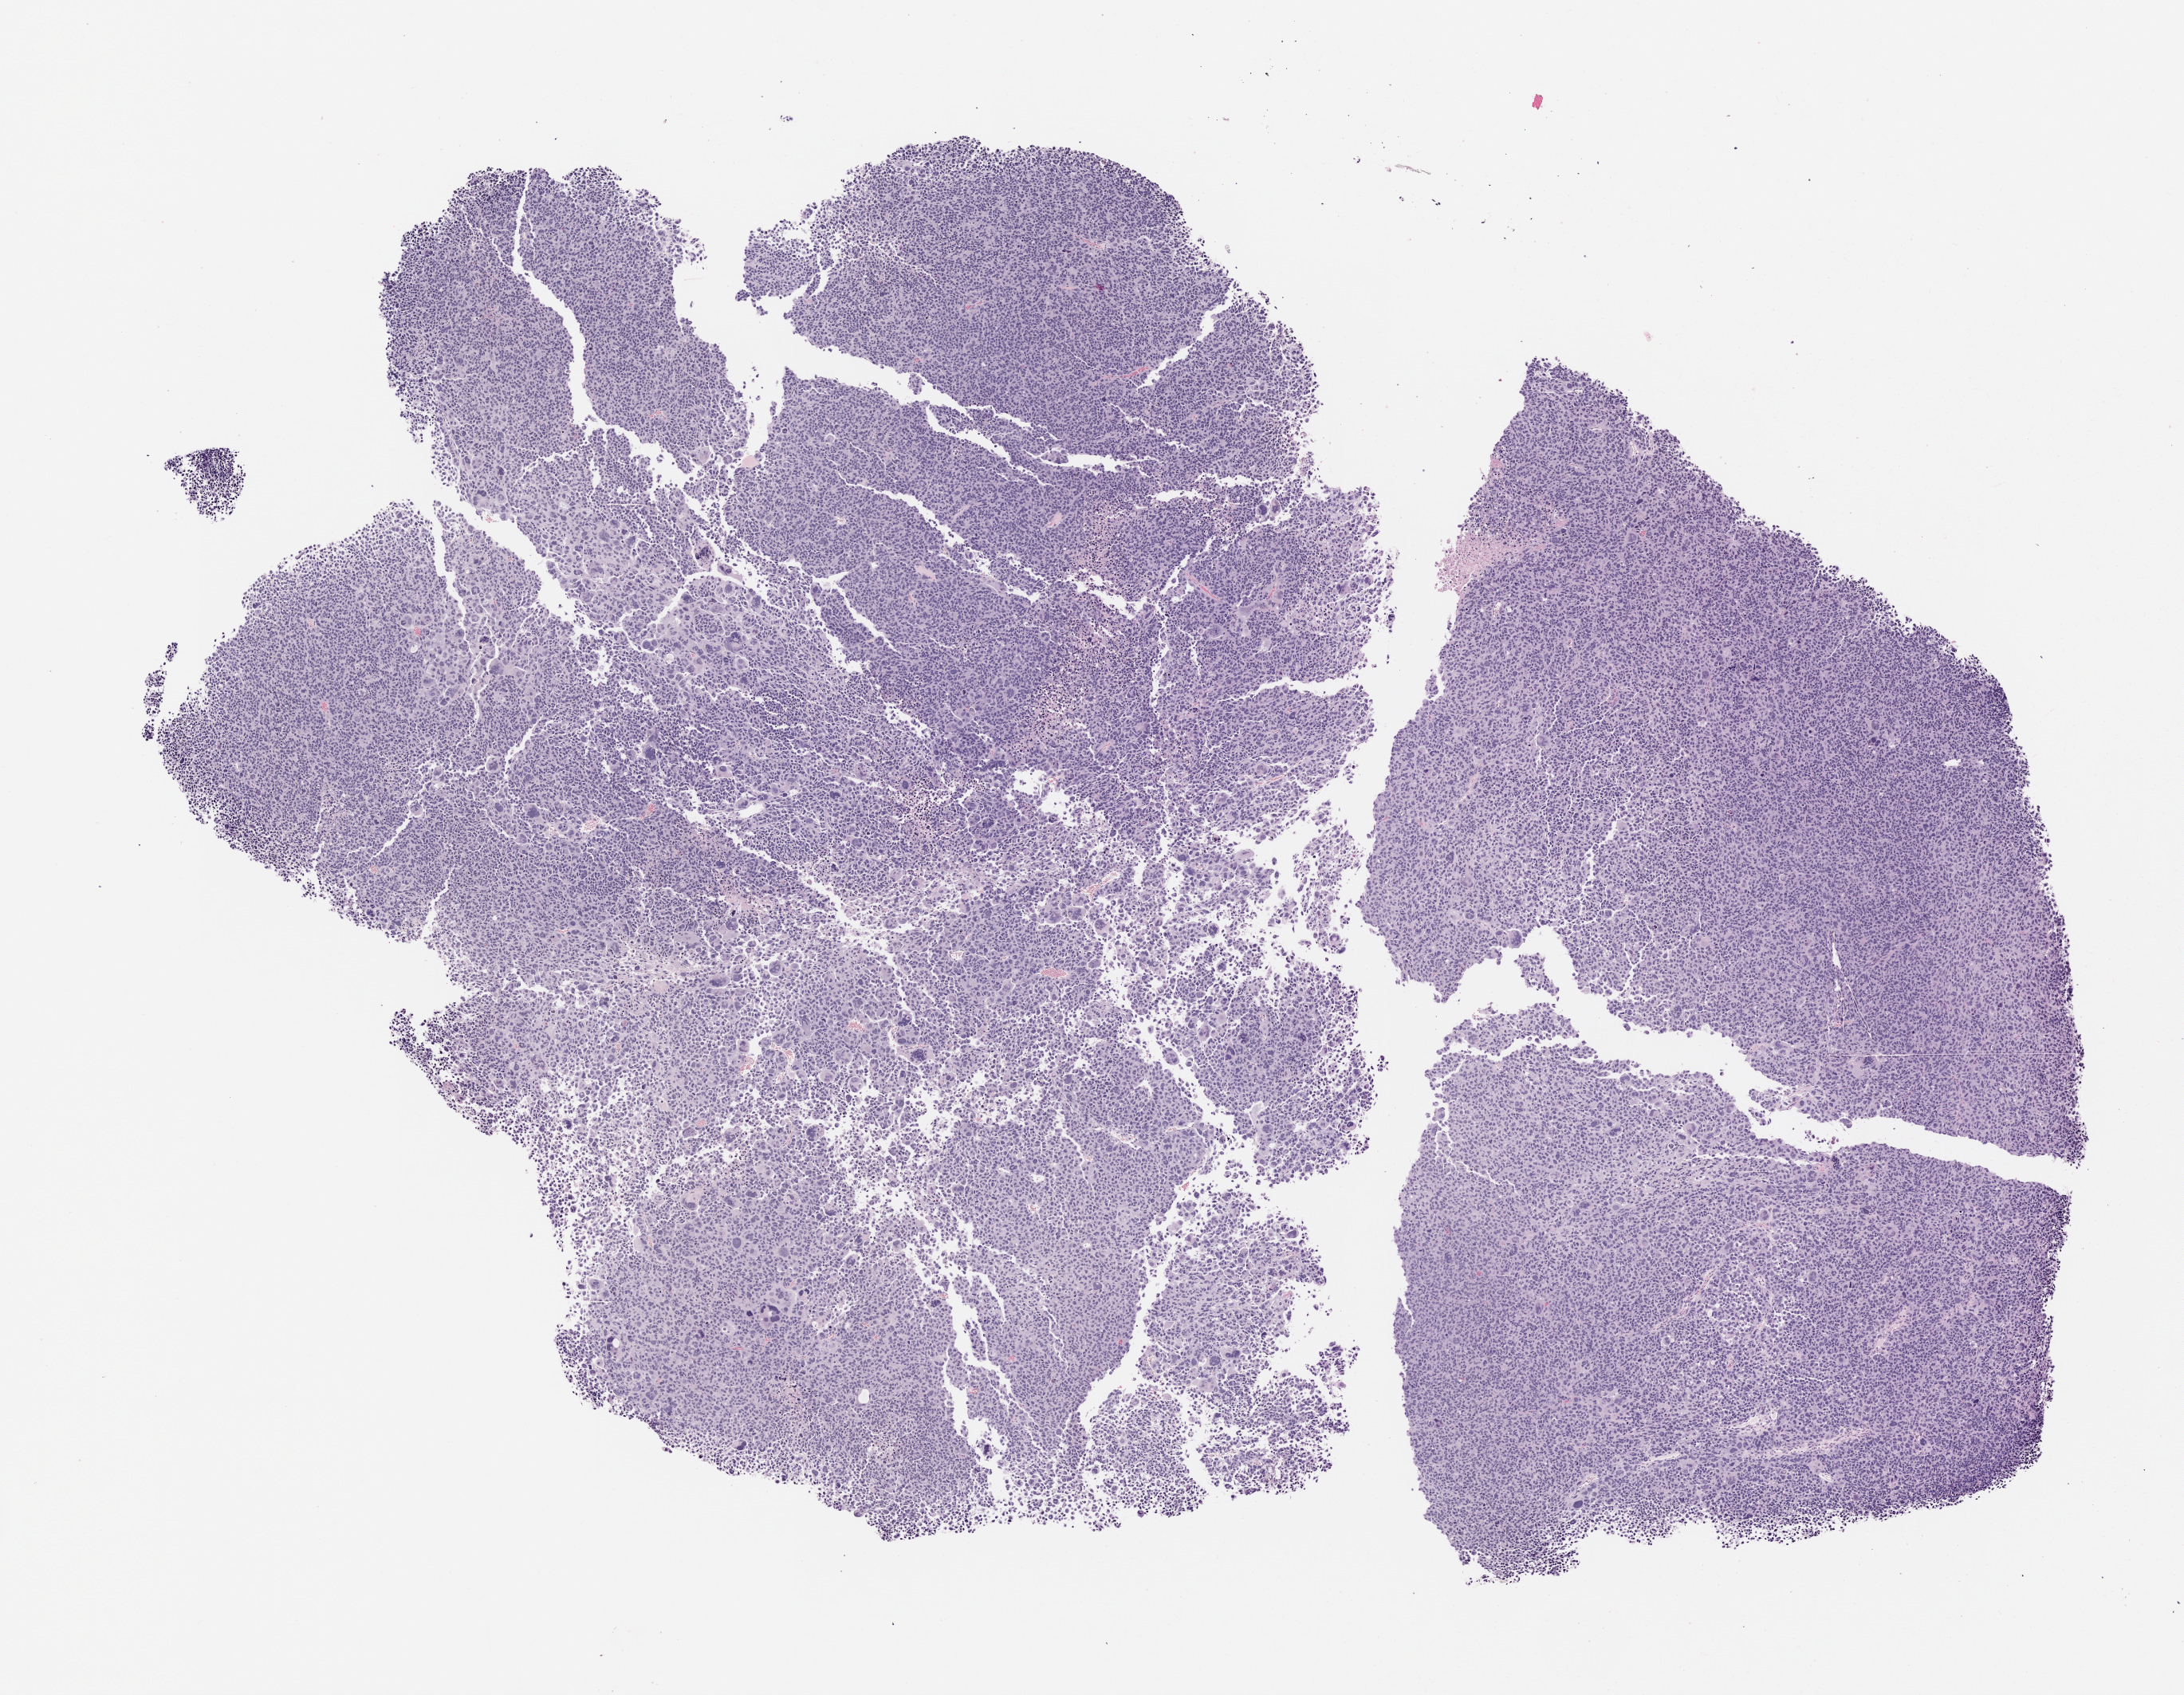
Whole-slide image, hematoxylin and eosin (H&E): patient-derived xenograft (human tumor grown in a mouse), passage 1 — whole scanned area (about 11.0 x 8.5 mm) shown as a low-resolution overview; formalin-fixed, paraffin-embedded (FFPE) tissue; tumor site category: skin.
* originating patient diagnosis: Melanoma